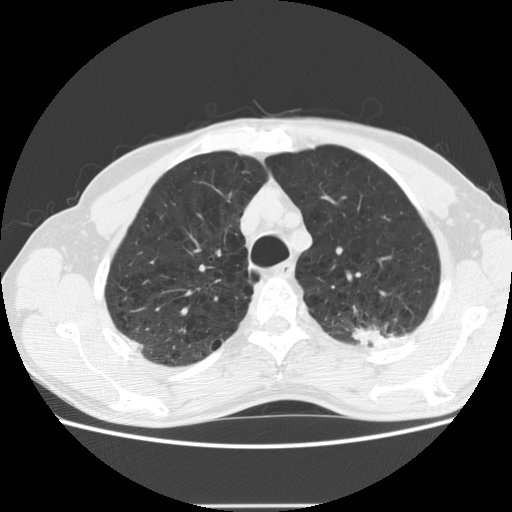
Low-dose screening chest CT, one axial slice. Position 153 of 191 along the scan axis. Lung window (W 1500 / L -600 HU). 512 × 512 image matrix.
Outlined on this slice (expert manual segmentation):
- lesion 1 (tumor, upper lobe of left lung): box from (x=353, y=327) to (x=387, y=345) px